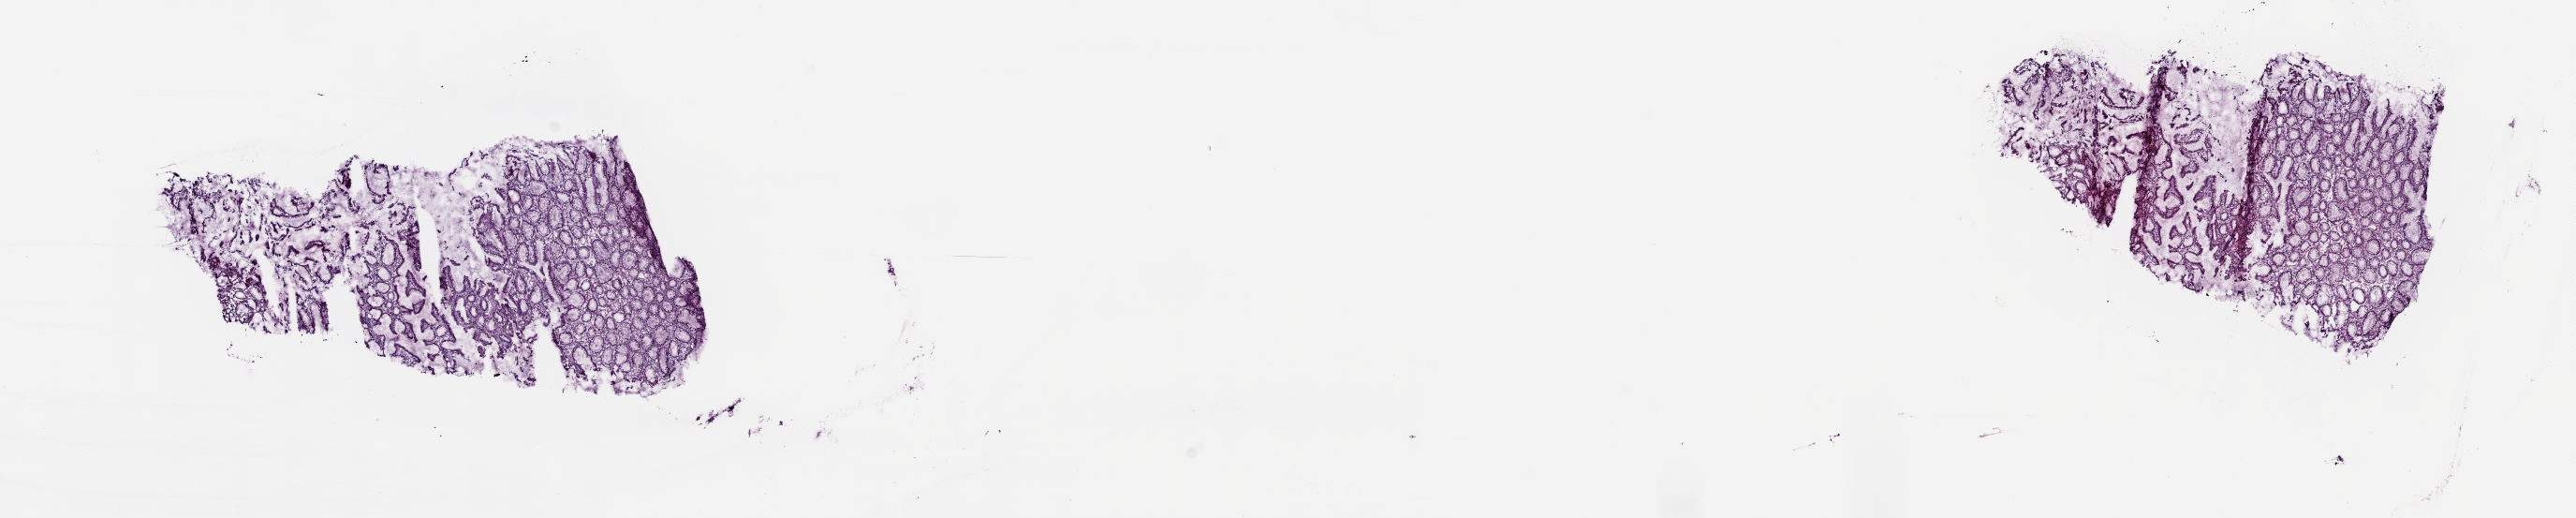
H&E-stained whole-slide image, a low-resolution overview of the entire scanned area, about 21.8 x 4.4 mm (from a 20x scan); frozen section from the top of the tissue portion; pancreas, solid tissue normal (non-tumour tissue) sample. Female patient; age at initial diagnosis 49 years. Pathologist review of this section (percent, as recorded): tumour cells 0%, tumour nuclei 0%, normal cells 80%, stromal cells 20%, necrosis 0%. Inflammatory infiltration, as recorded: lymphocyte infiltration 70%, monocyte infiltration 10%, neutrophil infiltration 10%.
This section: solid tissue normal sample (biorepository sample class). Patient diagnosis: Infiltrating duct carcinoma, NOS (head of pancreas).